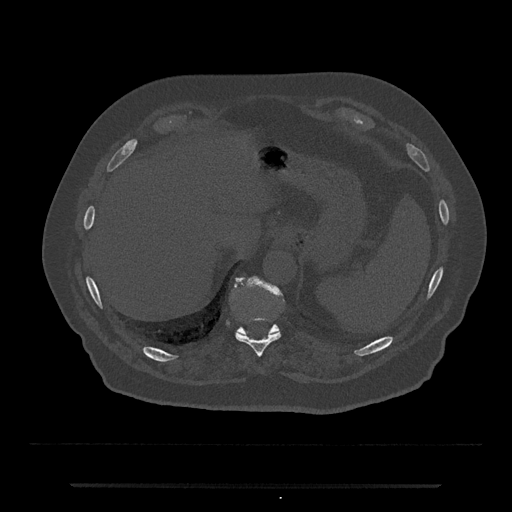
CT including the spine, one axial slice. Slice 689 of 797 in the series (ordered by position). Reconstruction kernel Br40s/3. 120 kVp. Bone window (W 1800 / L 400 HU). 512 × 512 image matrix, field of view 434 × 434 mm. Patient: male, 80 years. From the clinical record (not read from this slice): primary cancer: prostate.
Annotated regions visible in this slice (semi-automatic segmentation, software-assisted and operator-edited):
- T10 vertebra: box from (x=235, y=332) to (x=281, y=357) px
- T11 vertebra: (x=235, y=276)–(x=282, y=334)